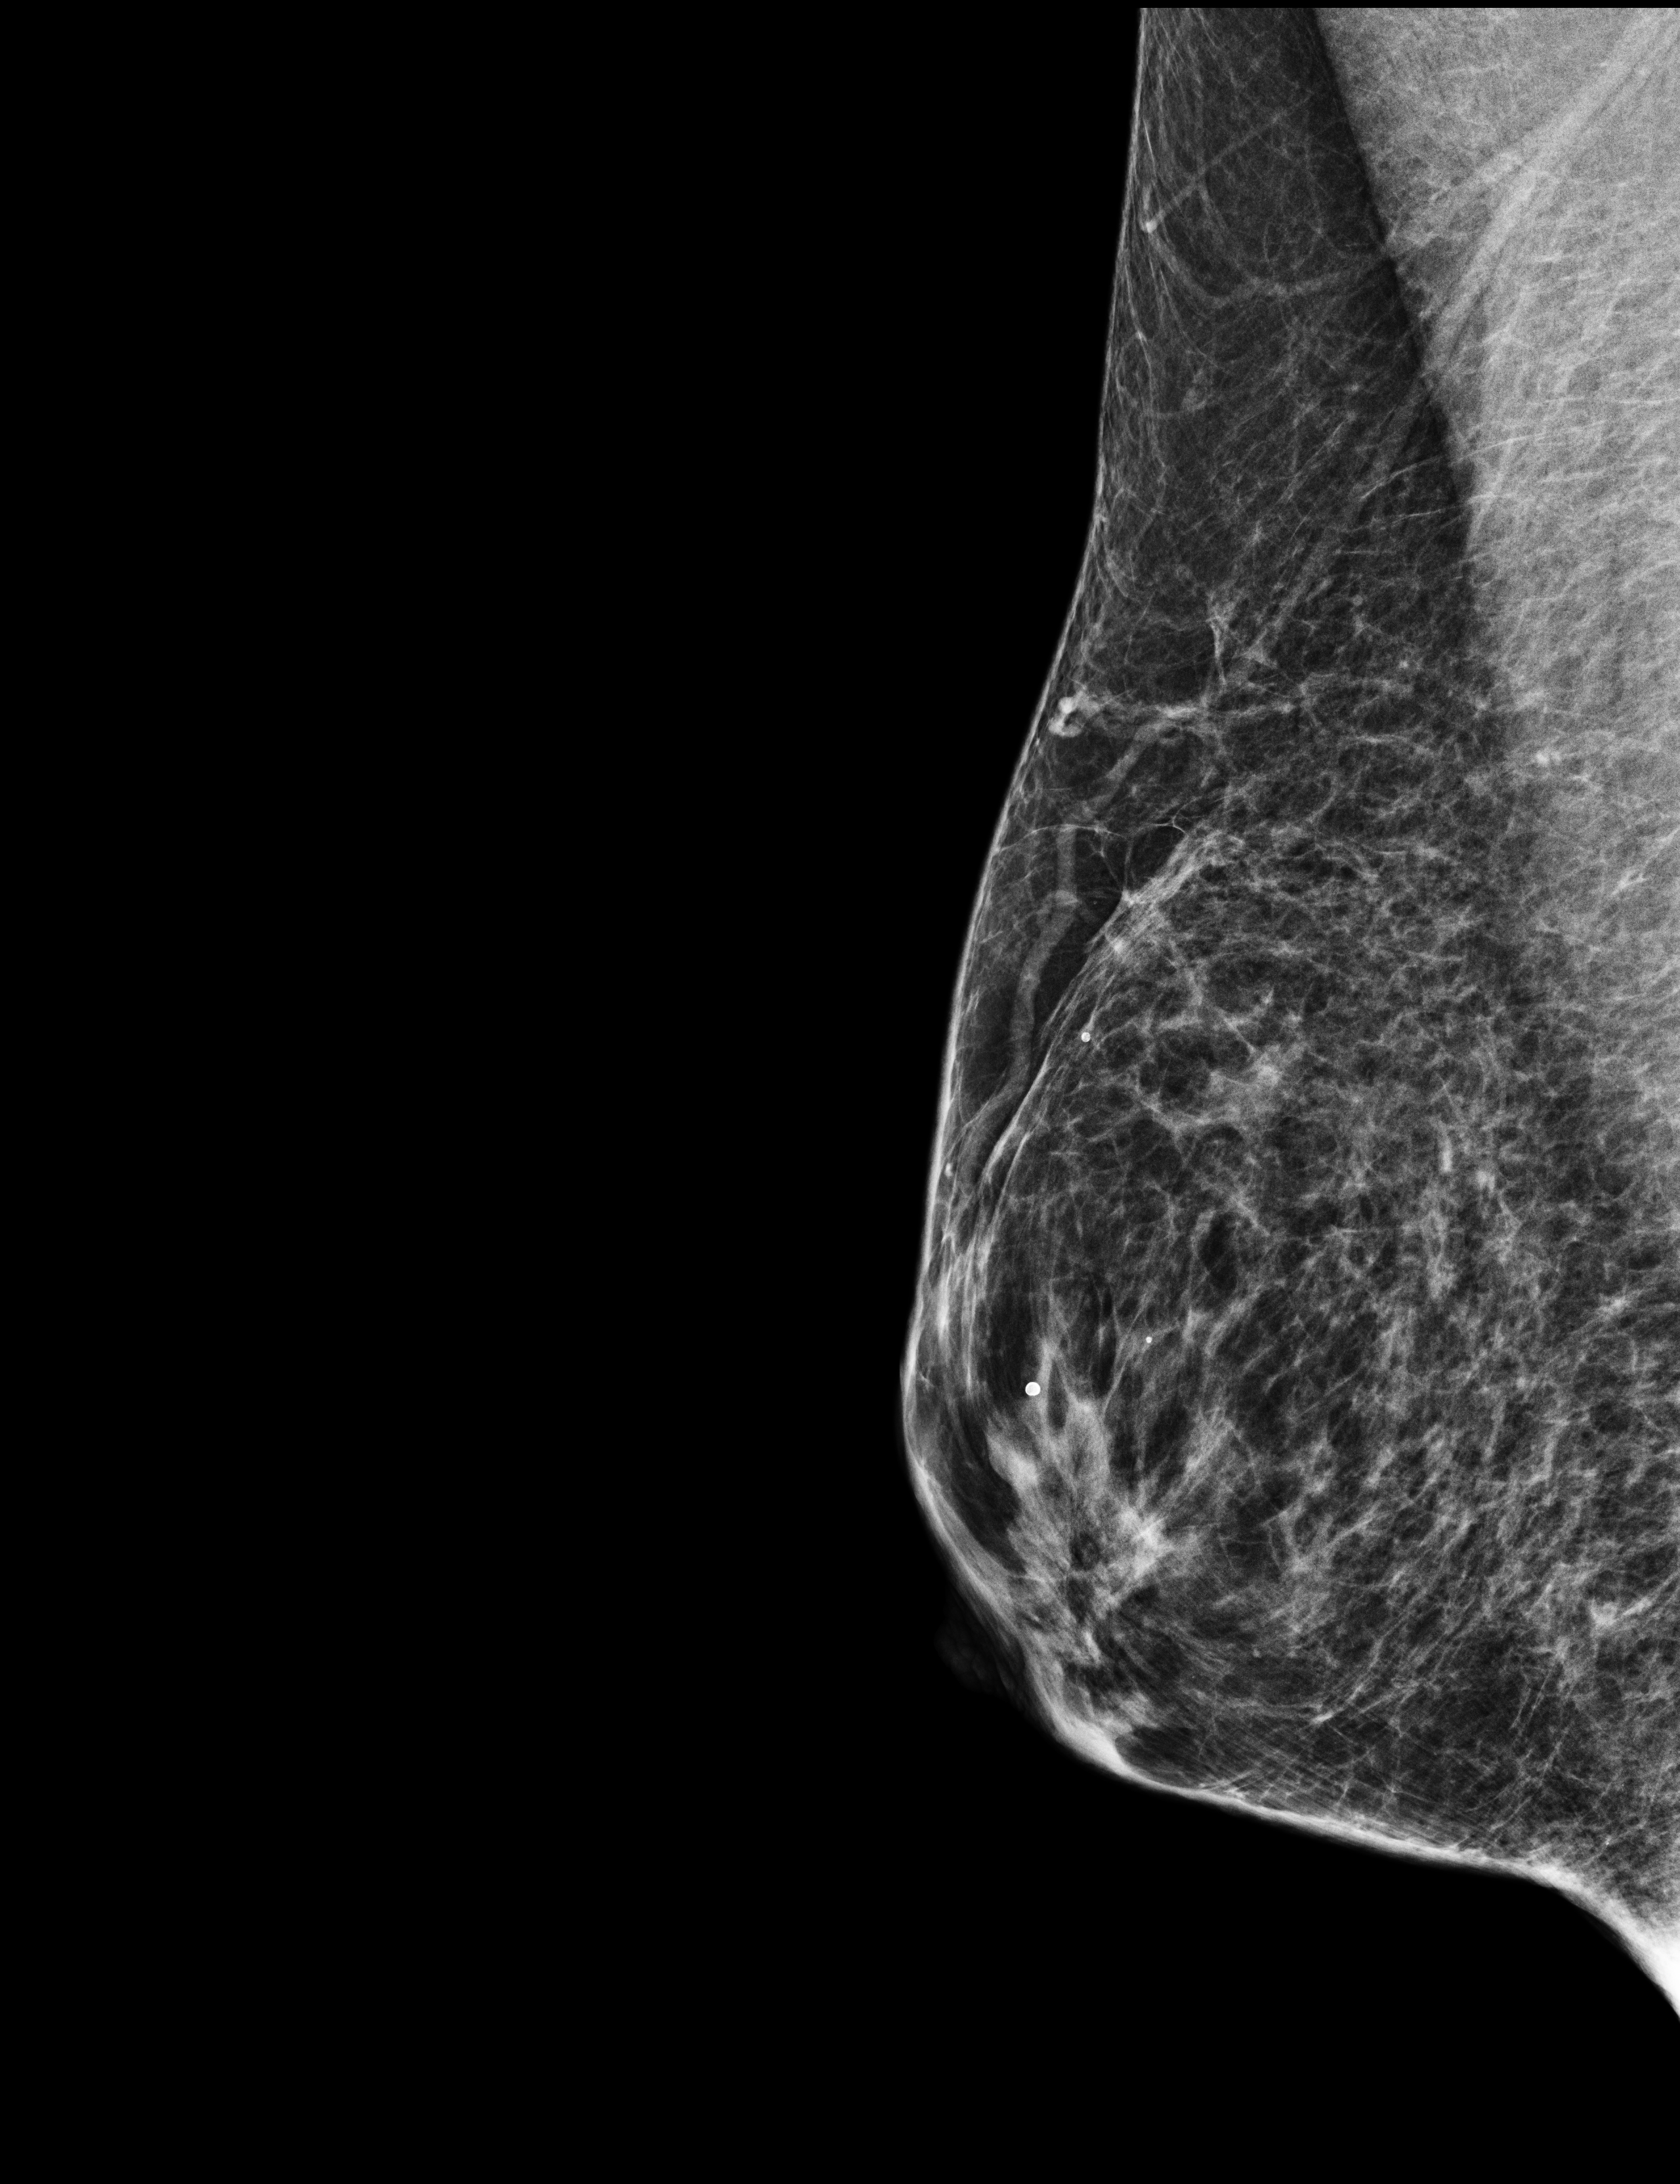
Full-field digital mammogram (FFDM), right breast, mediolateral oblique (MLO) view, annual screening mammography examination. Female patient, age 51 years.
Final BI-RADS category for the screening round (tomosynthesis exam, both breasts): category 2.